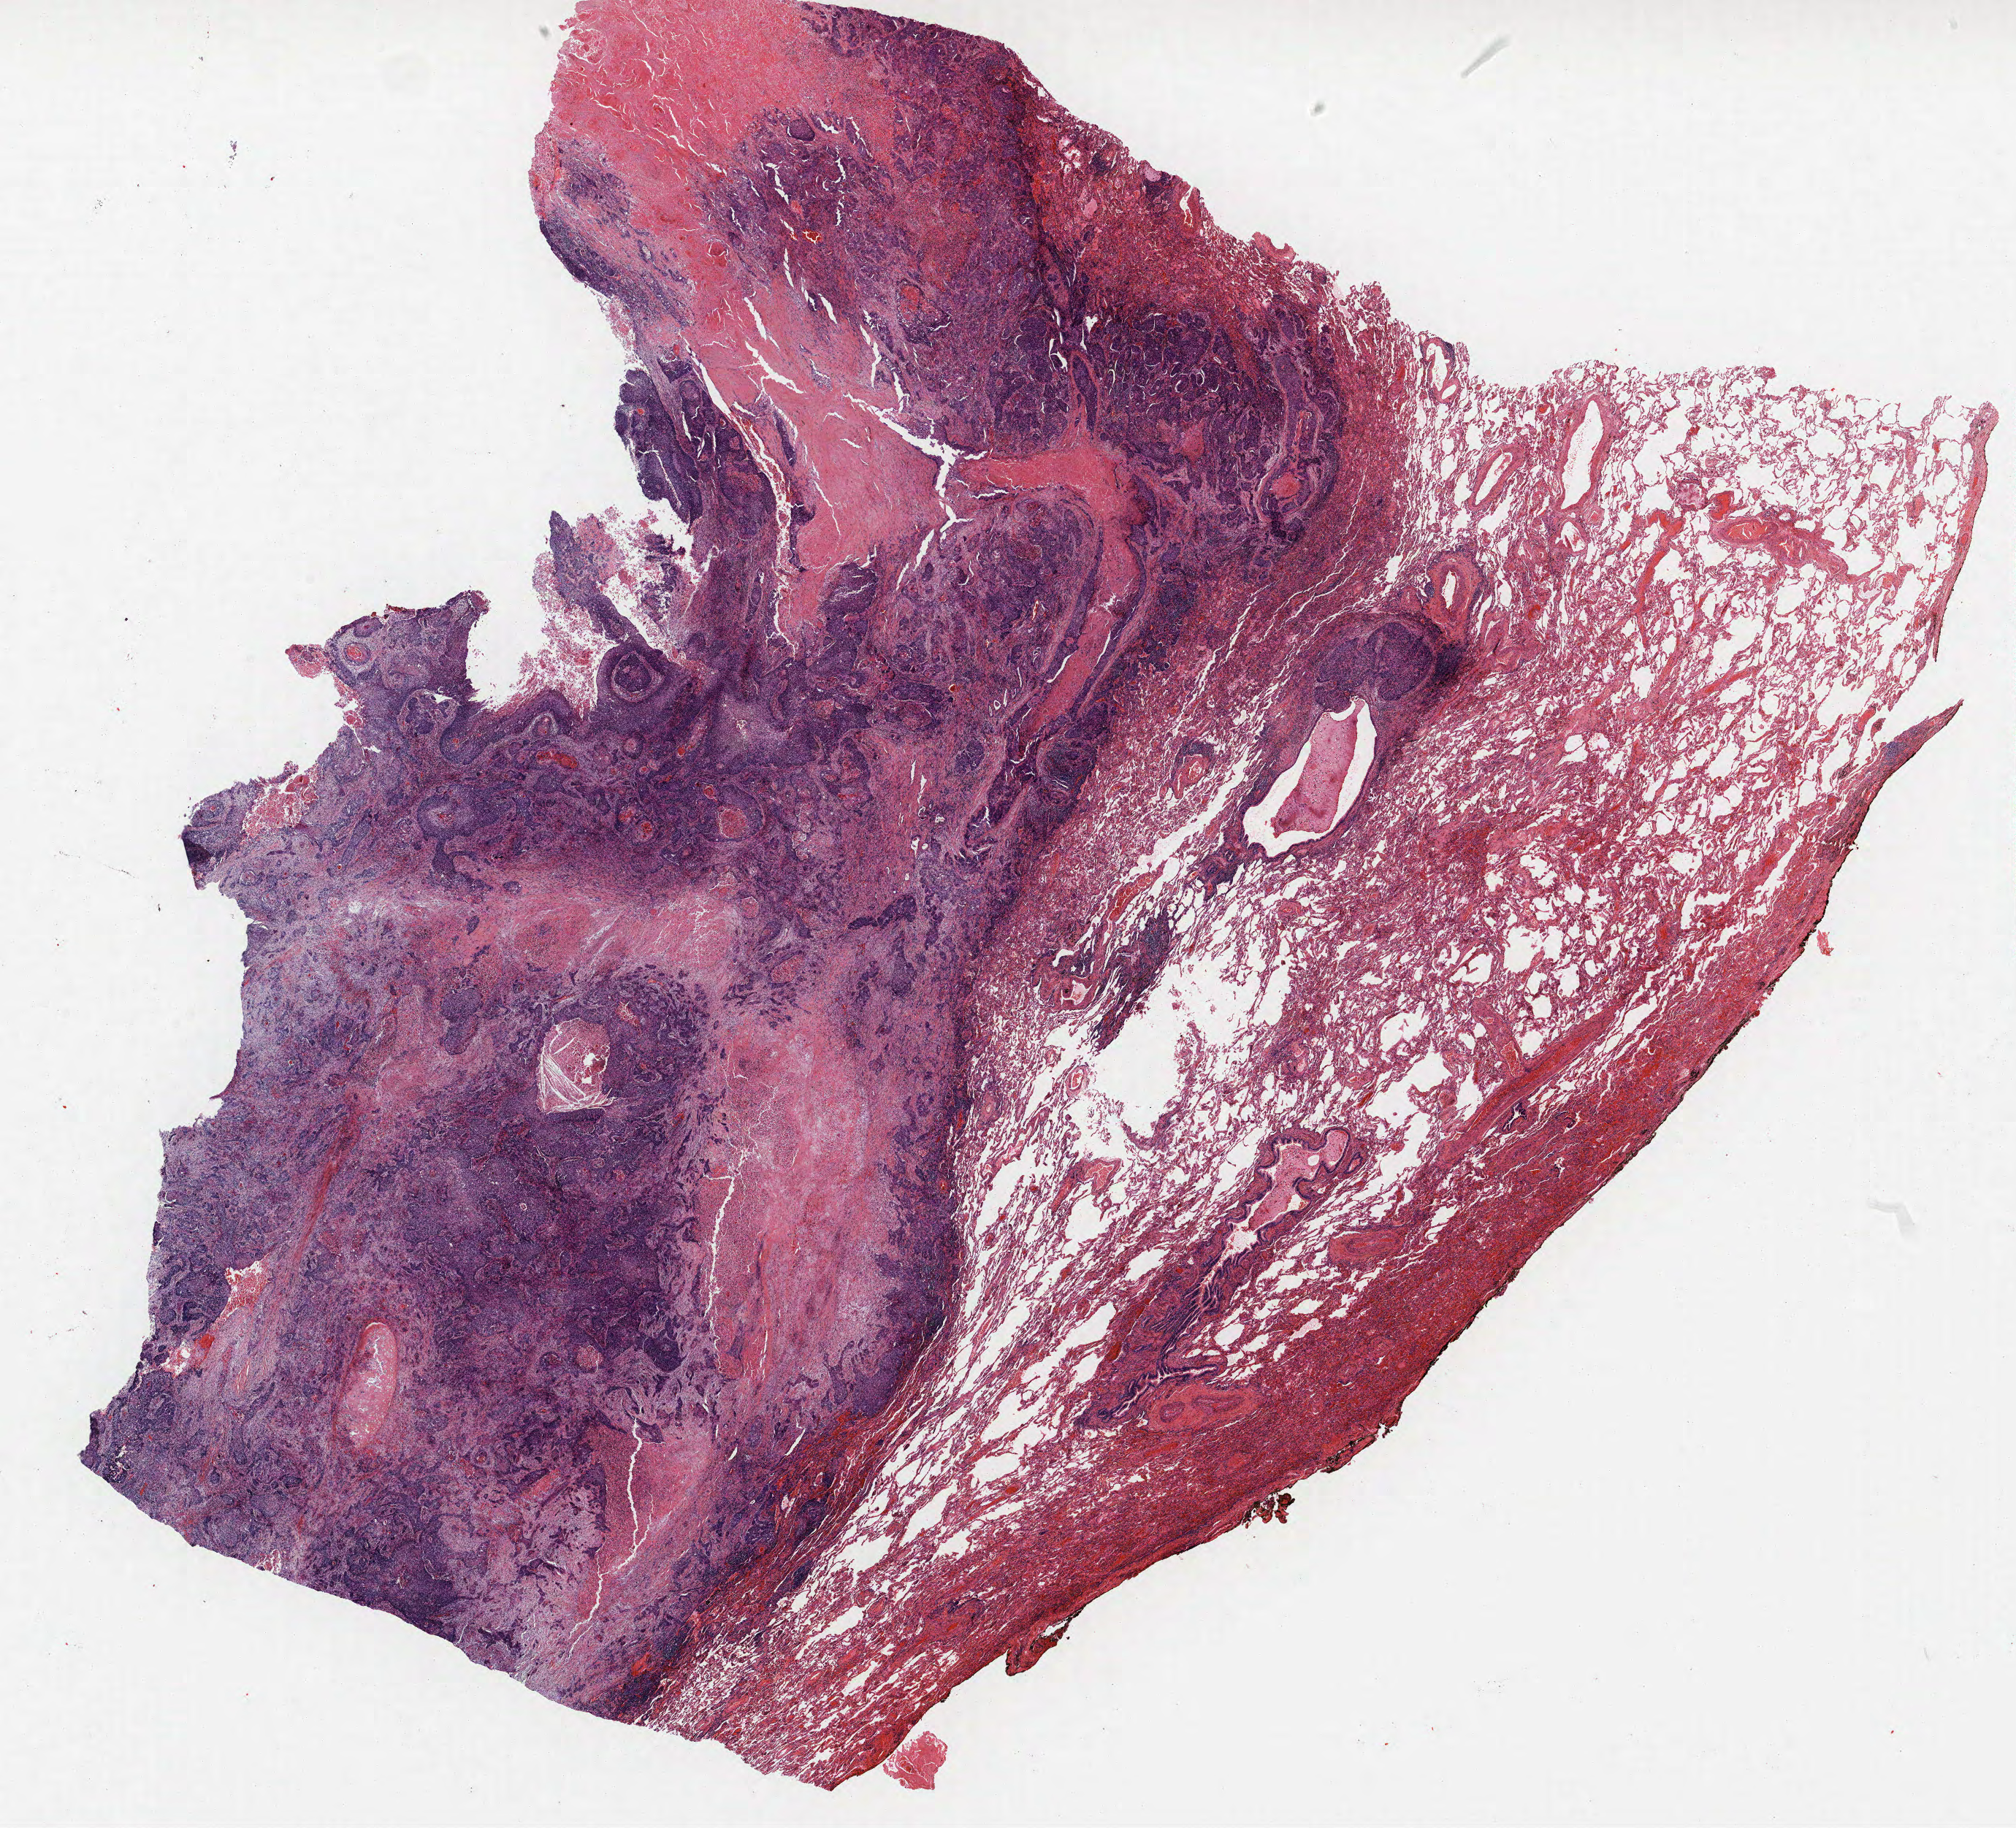
H&E whole-slide image, low-resolution overview of the scanned area, about 22.1 x 20.0 mm (acquisition: 40x scan), FFPE section, lung tissue. Male, age 57 at enrolment. Former smoker at enrolment. Grade: poorly differentiated (G3).
Stage (AJCC 6th edition): IIA. Tumour size (pathology): 30 mm. Primary tumour location (clinical record): right upper lobe. Participant's lung-cancer diagnosis: Squamous cell carcinoma, NOS.